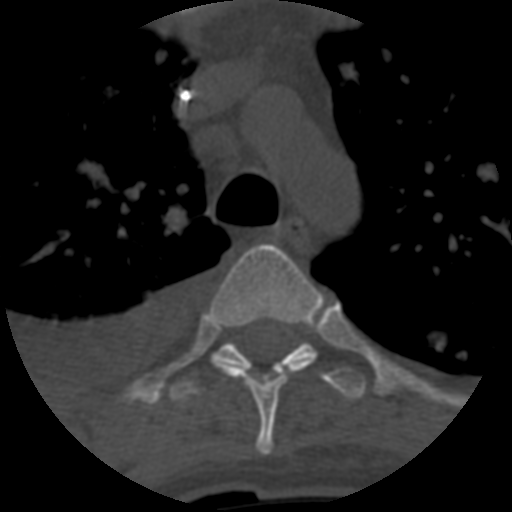
CT including the spine, one axial slice. Slice 464 of 708 in the series (ordered by position). 120 kVp. One of 3 acquisitions stored at this slice position. Bone window (W 1800 / L 400 HU). 512 × 512 image matrix, field of view 160 × 160 mm. Patient age 55 years. Case-level facts recorded for this patient, not image findings: primary cancer: colon; vertebrae with lytic lesions (as recorded): T12, L1, L5.
Outlined on this slice (semi-automatic segmentation, software-assisted and operator-edited):
- T4 vertebra: bounding box (x1, y1, x2, y2) in pixels: (214, 244, 317, 455)
- T5 vertebra: (169, 342, 366, 404)